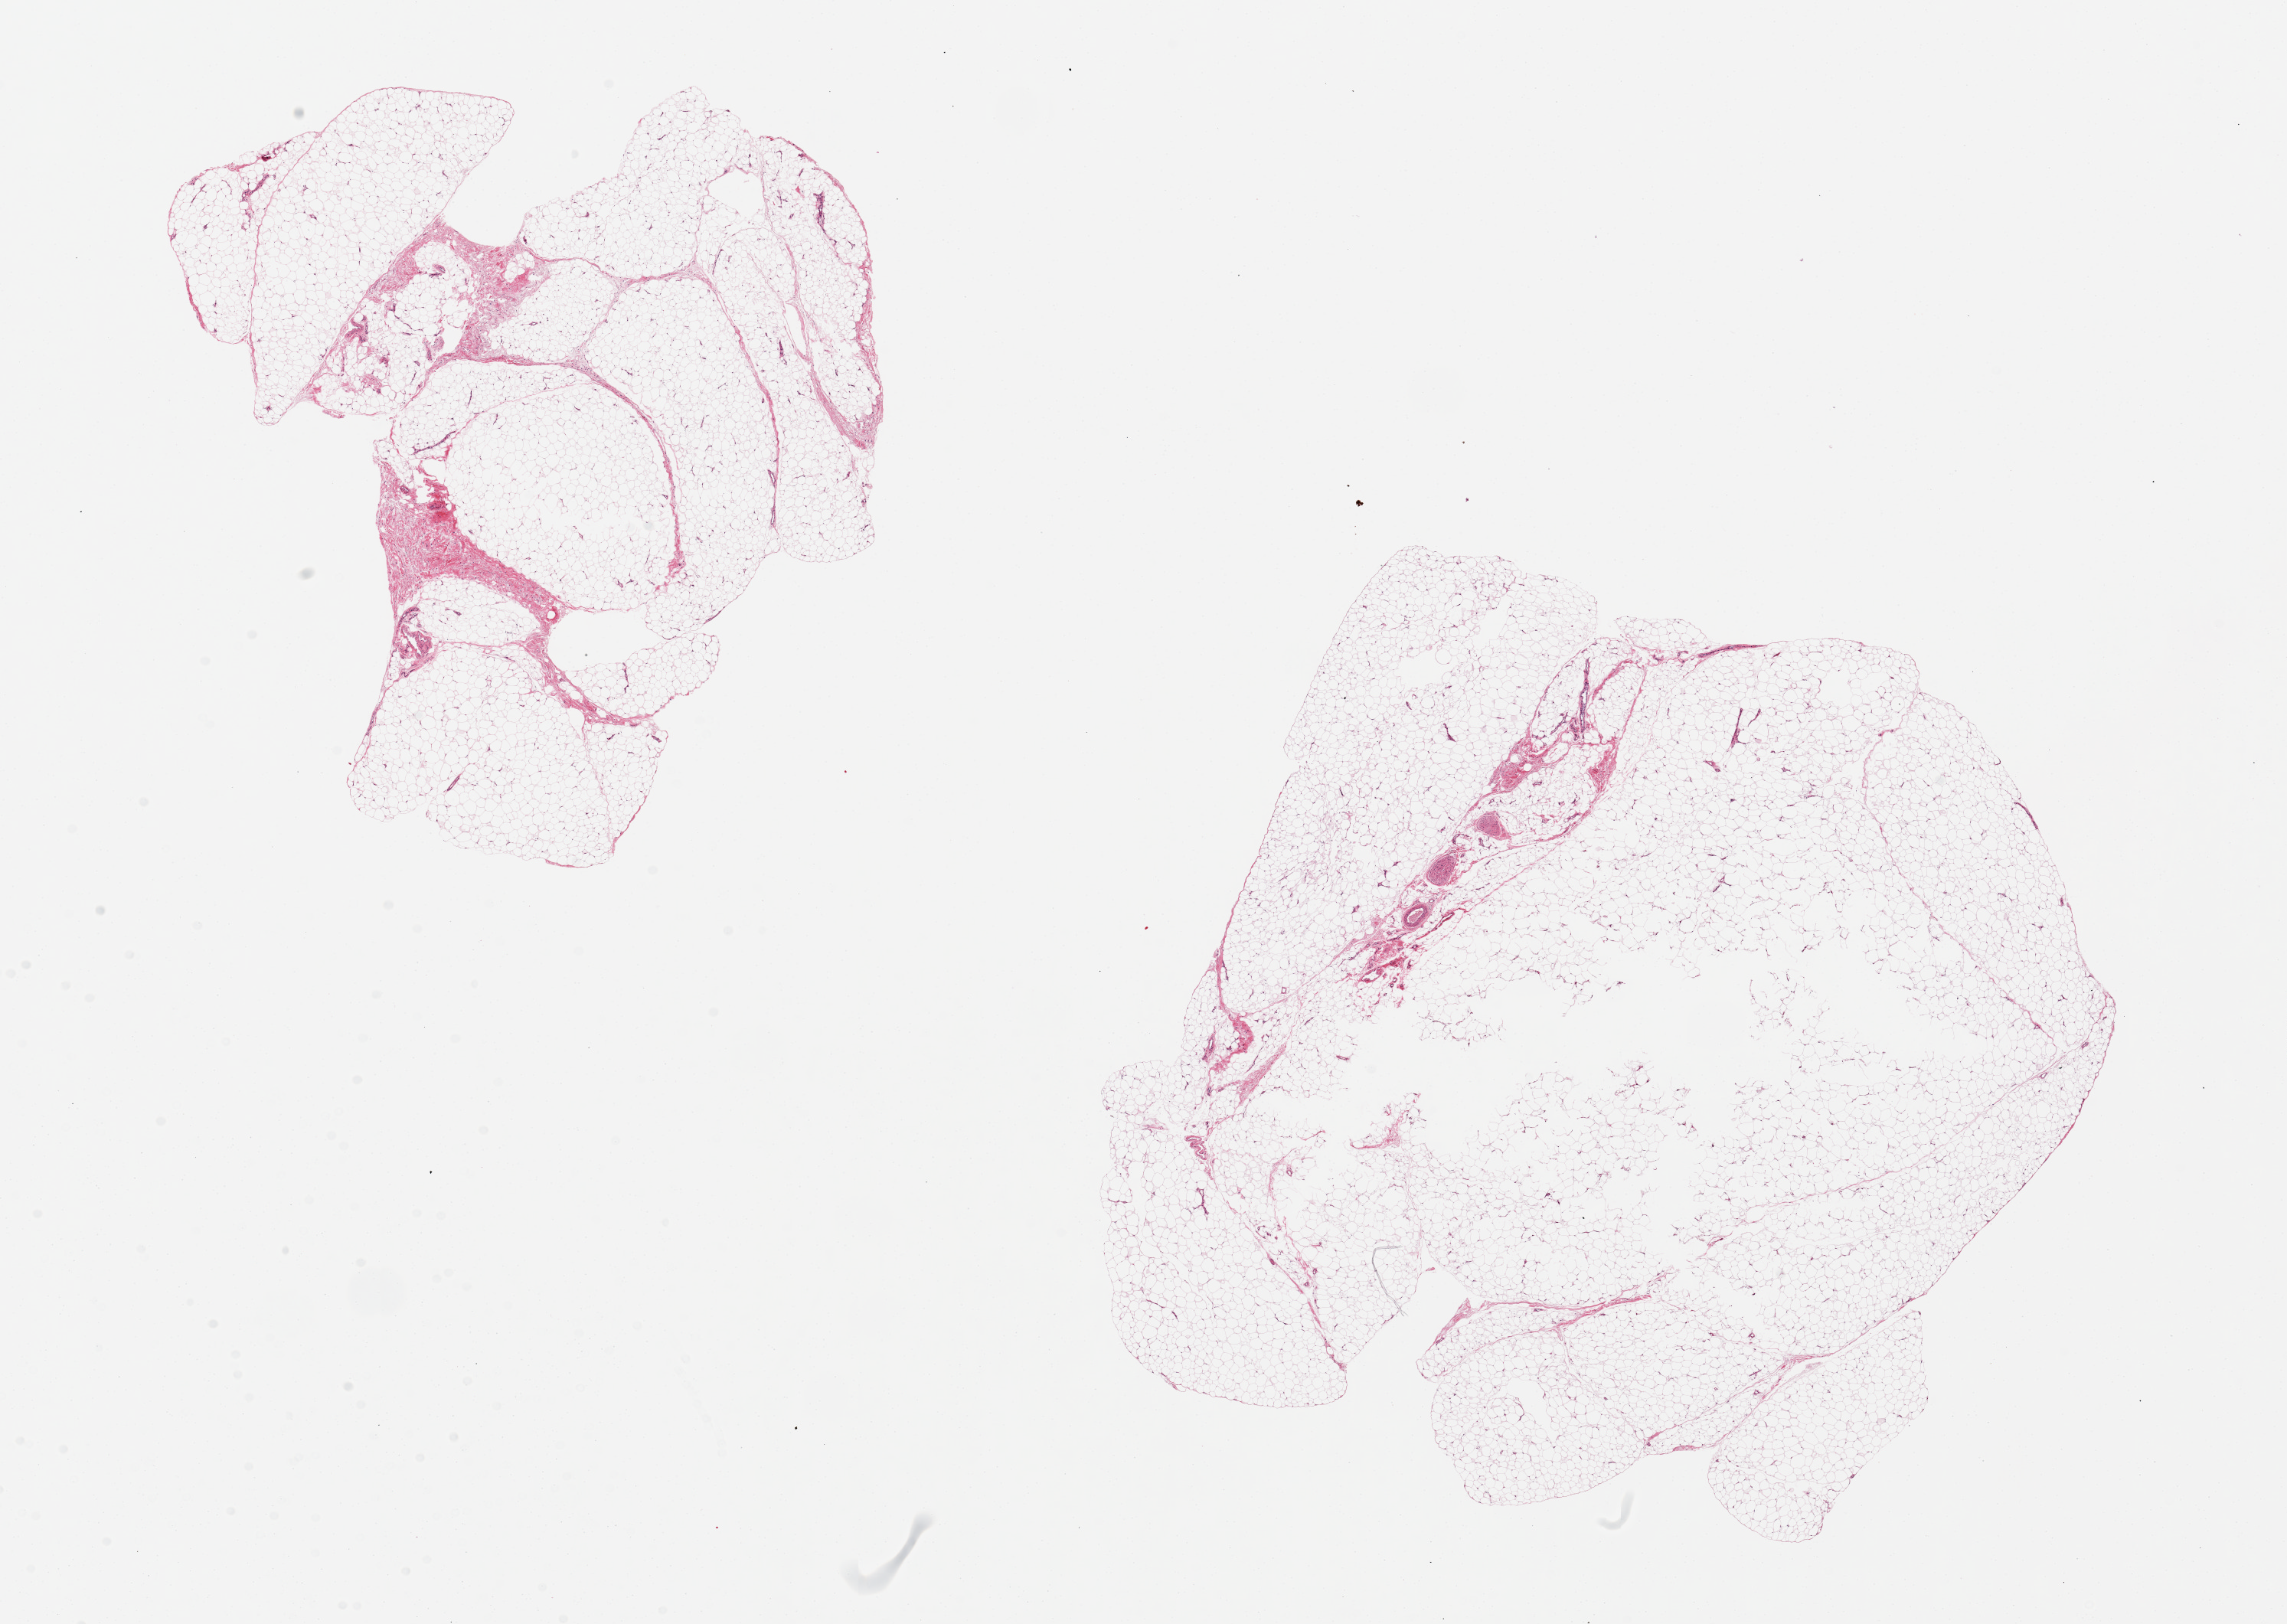
Digitized H&E-stained section, low-resolution overview of the scanned area, about 23.6 x 16.8 mm (from a 20x scan); PAXgene-fixed, paraffin-embedded tissue; sampled site (target tissue): adipose tissue; donor tissue sample. Donor: male.
Review note (as recorded): 2 aliquots, ~9x9mm.